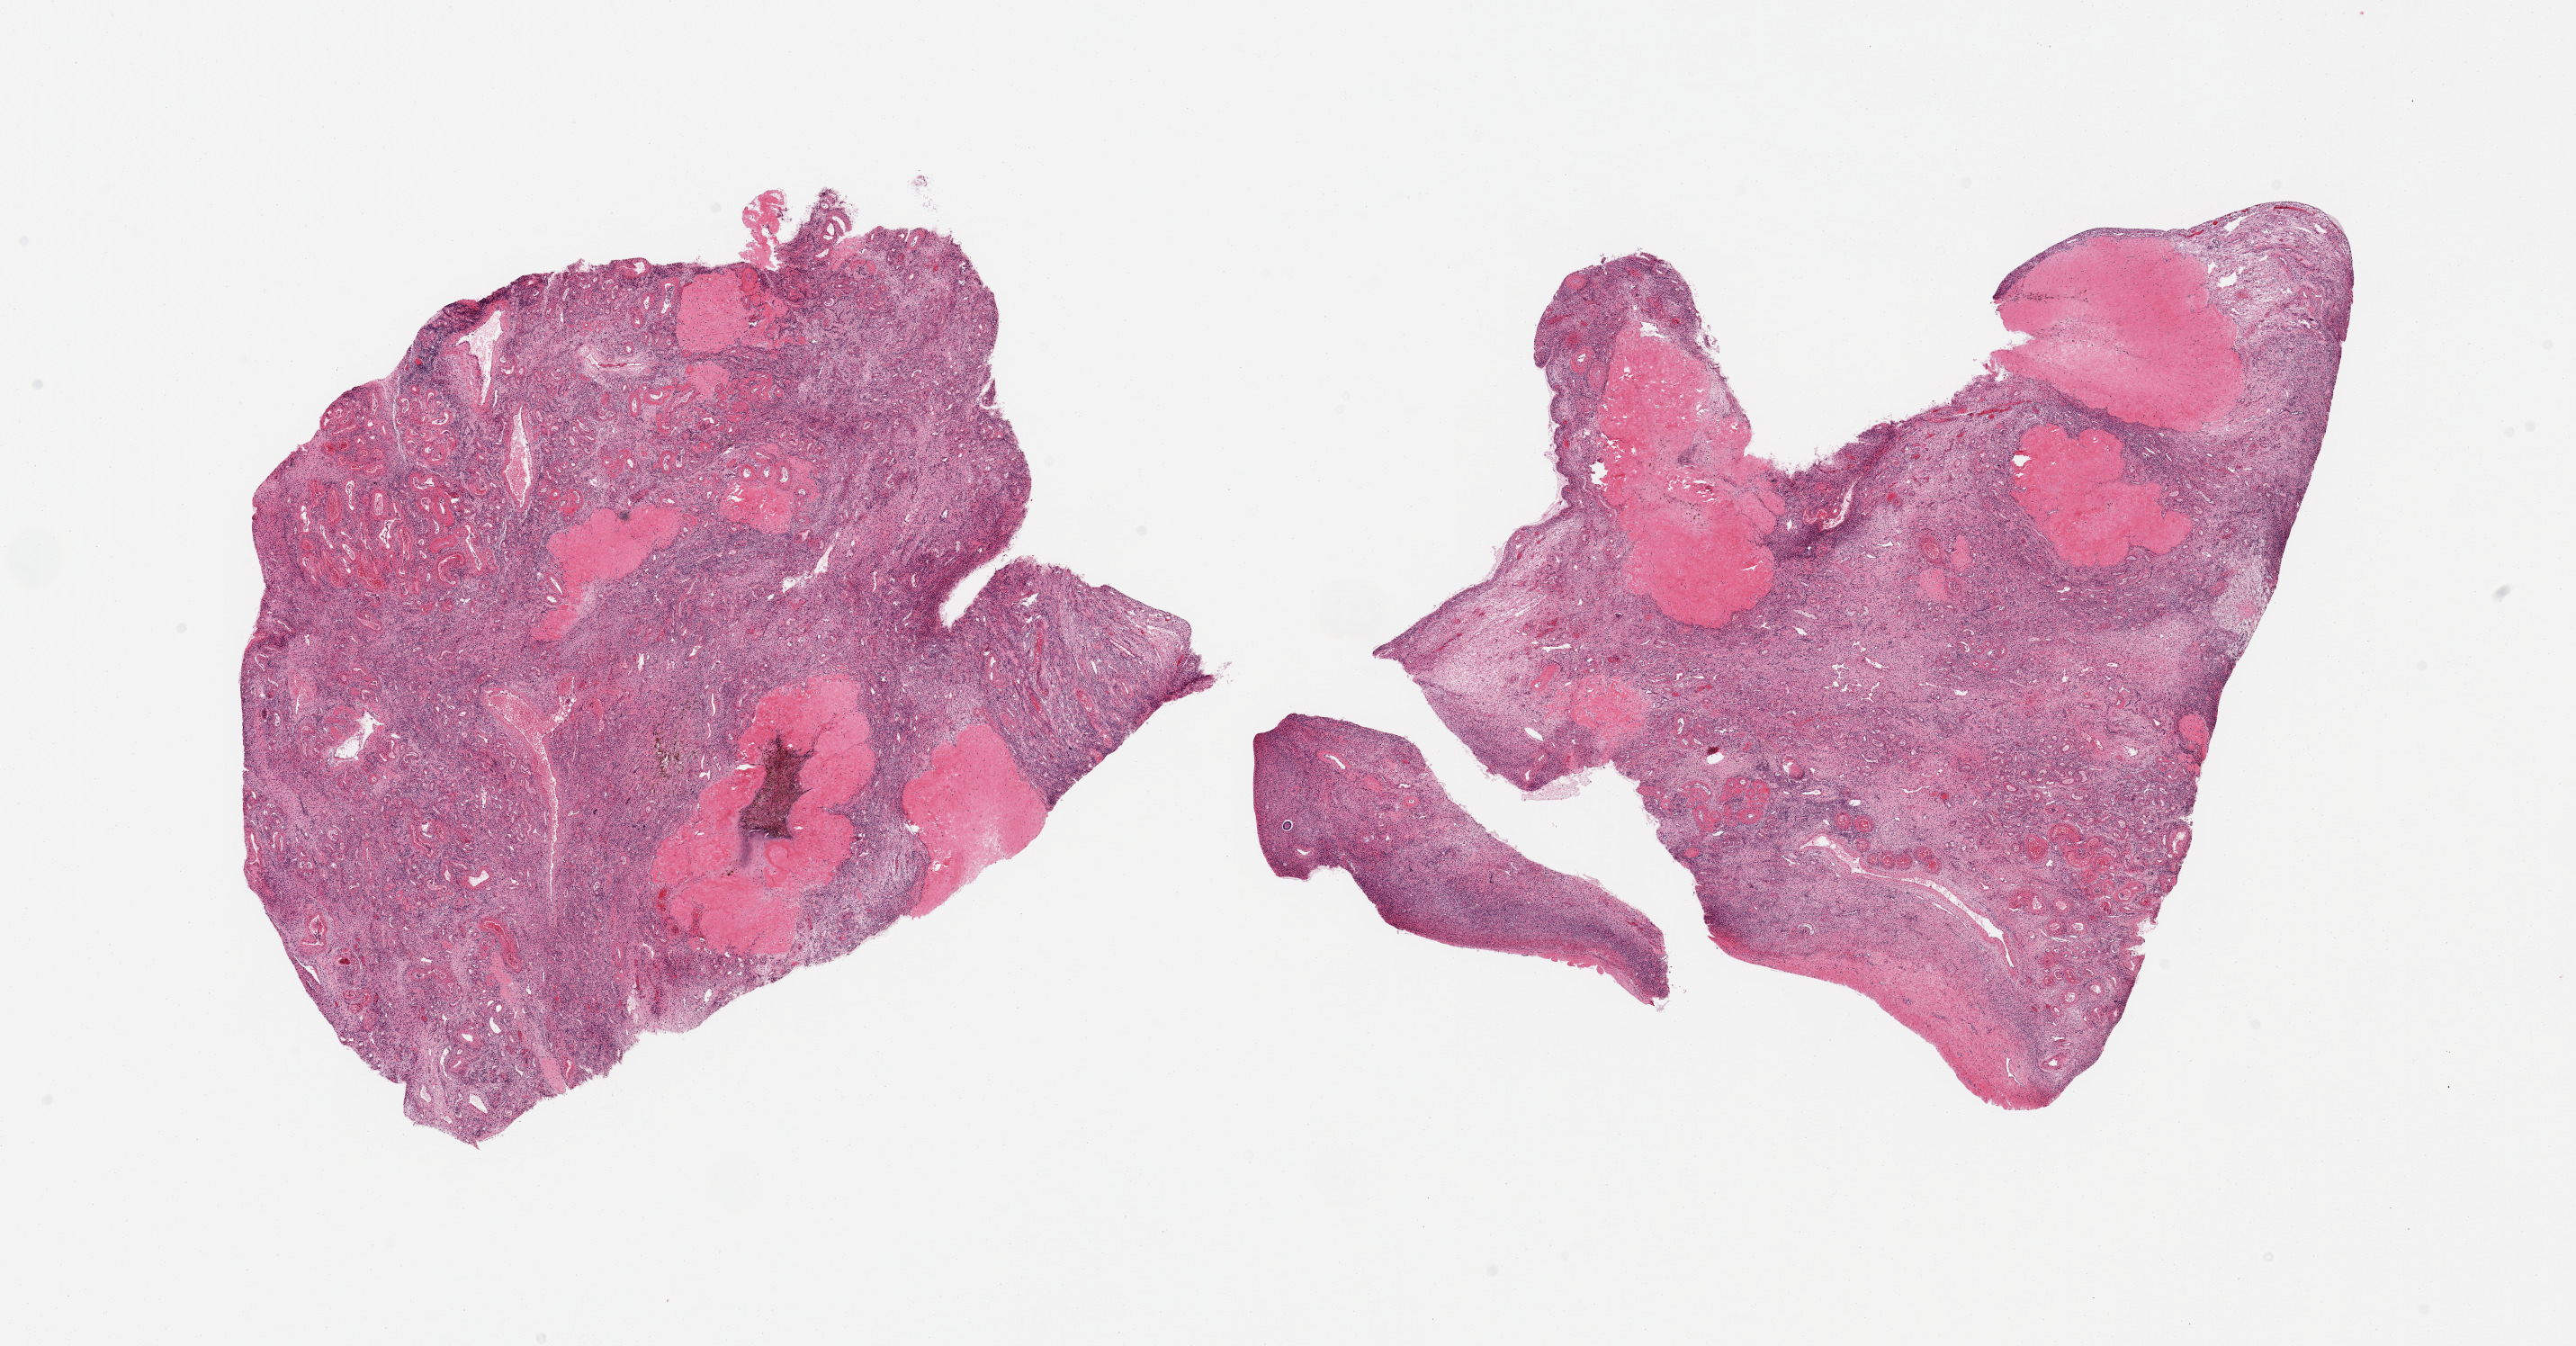
H&E whole-slide image, whole scanned area (about 22.6 x 11.8 mm) shown as a low-resolution overview. PAXgene-fixed paraffin-embedded (PFPE) section. Sampled site (target tissue): ovary. Tissue donor sample. Donor sex: female.
Reviewer comment on this tissue sample: 2 pieces, prominent corpora albicantia.